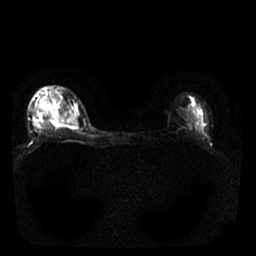
Breast MRI, one axial slice; slice 18 of 25 in the series (ordered by position); diffusion-weighted series; image 2 of 4 stored at this slice position (different b-values; order by instance number); 1.5 T; 256 × 256 image matrix, field of view 310 × 310 mm. Female patient.
Structures marked on this image (outlined manually by an expert reader):
- tumour on diffusion-weighted imaging: bounding box (x1, y1, x2, y2) in pixels: (40, 105, 76, 120)